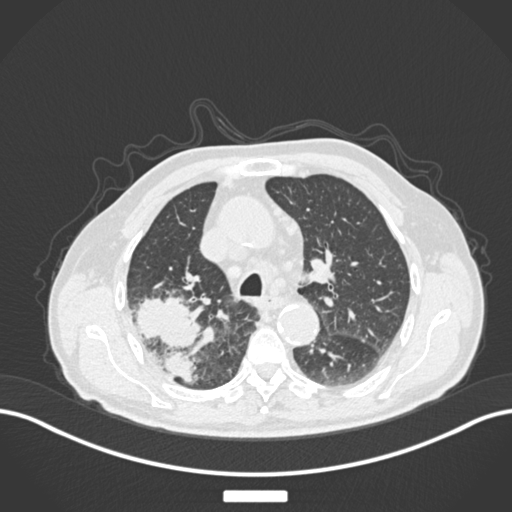
Chest CT, one axial slice. Position 126 of 201 along the scan axis. Lung window (W 1500 / L -600 HU). 1 mm slice thickness. 512 × 512 image matrix. Patient: male, 72 years. From the clinical record (not read from this slice): clinical TNM (as recorded): T3 N2 M0.
Outlined on this slice (rectangle marked by the reading radiologist):
- lung tumour (recorded histology: adenocarcinoma): bounding box [x1, y1, x2, y2] px = [131, 289, 206, 387]